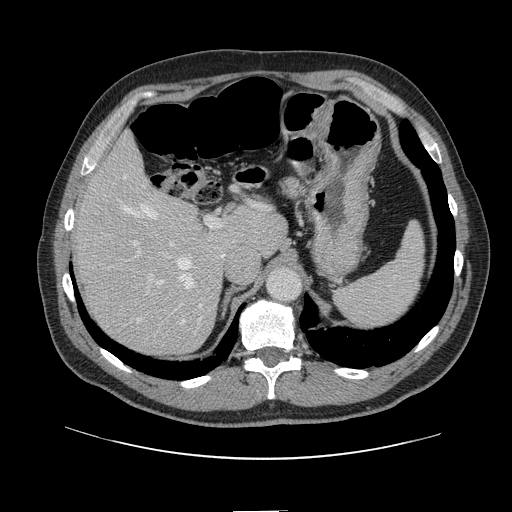
Contrast-enhanced abdominal CT, one axial slice. Slice 95 of 161 in the series (ordered by position). 120 kVp. Intravenous contrast given. Soft-tissue window (W 400 / L 40 HU). 2.5 mm slice thickness. 512 × 512 image matrix, field of view 412 × 412 mm. Male patient, age 66 years. Case-level facts recorded for this patient, not image findings: diagnosis: colorectal cancer liver metastases, imaged before liver resection; multiple liver metastases: no; largest metastasis: 3.5 cm; disease in both lobes: no.
Structures marked on this image (expert manual segmentation):
- hepatic veins: bounding box (x1, y1, x2, y2) in pixels: (120, 176, 193, 322)
- liver: (79, 138, 285, 354)
- planned liver remnant (the part of the liver to remain after resection): (79, 137, 285, 304)
- portal vein (with intrahepatic branches): (119, 216, 222, 314)